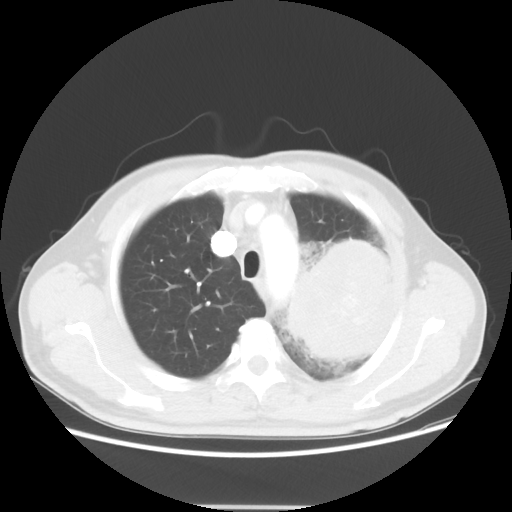
Chest CT, one axial slice; position 43 of 53 along the scan axis; 100 kVp; lung window (W 1500 / L -600 HU); 5 mm slice thickness; 512 × 512 image matrix, field of view 391 × 391 mm. Patient: male, 60 years. Case-level facts recorded for this patient, not image findings: clinical TNM (as recorded): T4 N1 M1a; histopathological grade: G3.
Annotated regions visible in this slice (bounding box drawn by a radiologist):
- lung tumour (recorded histology: large cell carcinoma): bounding box [x1, y1, x2, y2] px = [290, 225, 398, 368]